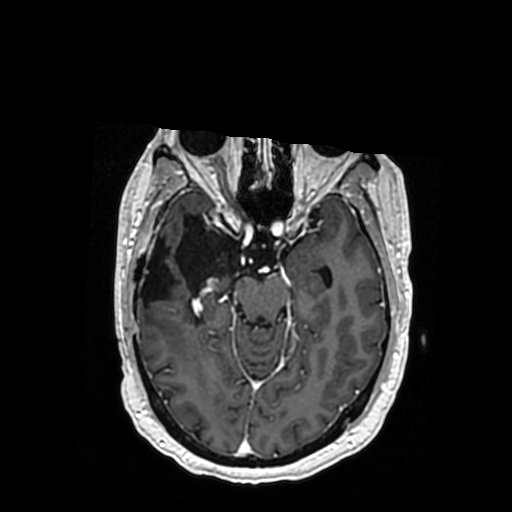
Brain MRI from a brain-tumour surgery series, one axial slice. T1-weighted post-contrast. 0.5 mm slice thickness. 512 × 512 image matrix, field of view 260 × 260 mm. Case-level facts recorded for this patient, not image findings: histopathology: Oligodendroglioma; WHO grade: 3; IDH mutation: yes.
Structures marked on this image (manually delineated by an expert):
- previous resection cavity: bounding box [x1, y1, x2, y2] px = [140, 215, 240, 319]